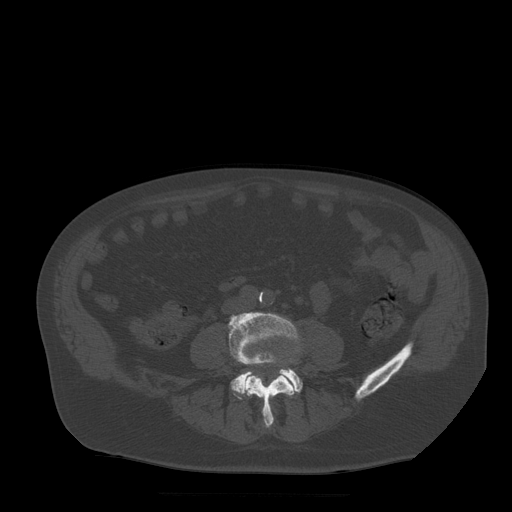
CT including the spine, one axial slice. Position 106 of 522 along the scan axis. Bone window (W 1800 / L 400 HU). 1.25 mm slice thickness. 512 × 512 image matrix. Patient age 72 years. From the clinical record (not read from this slice): primary cancer: prostate.
Structures marked on this image (semi-automatically segmented with operator editing):
- L4 vertebra: box from (x=229, y=313) to (x=301, y=428) px
- L5 vertebra: (x=232, y=364)–(x=303, y=400)